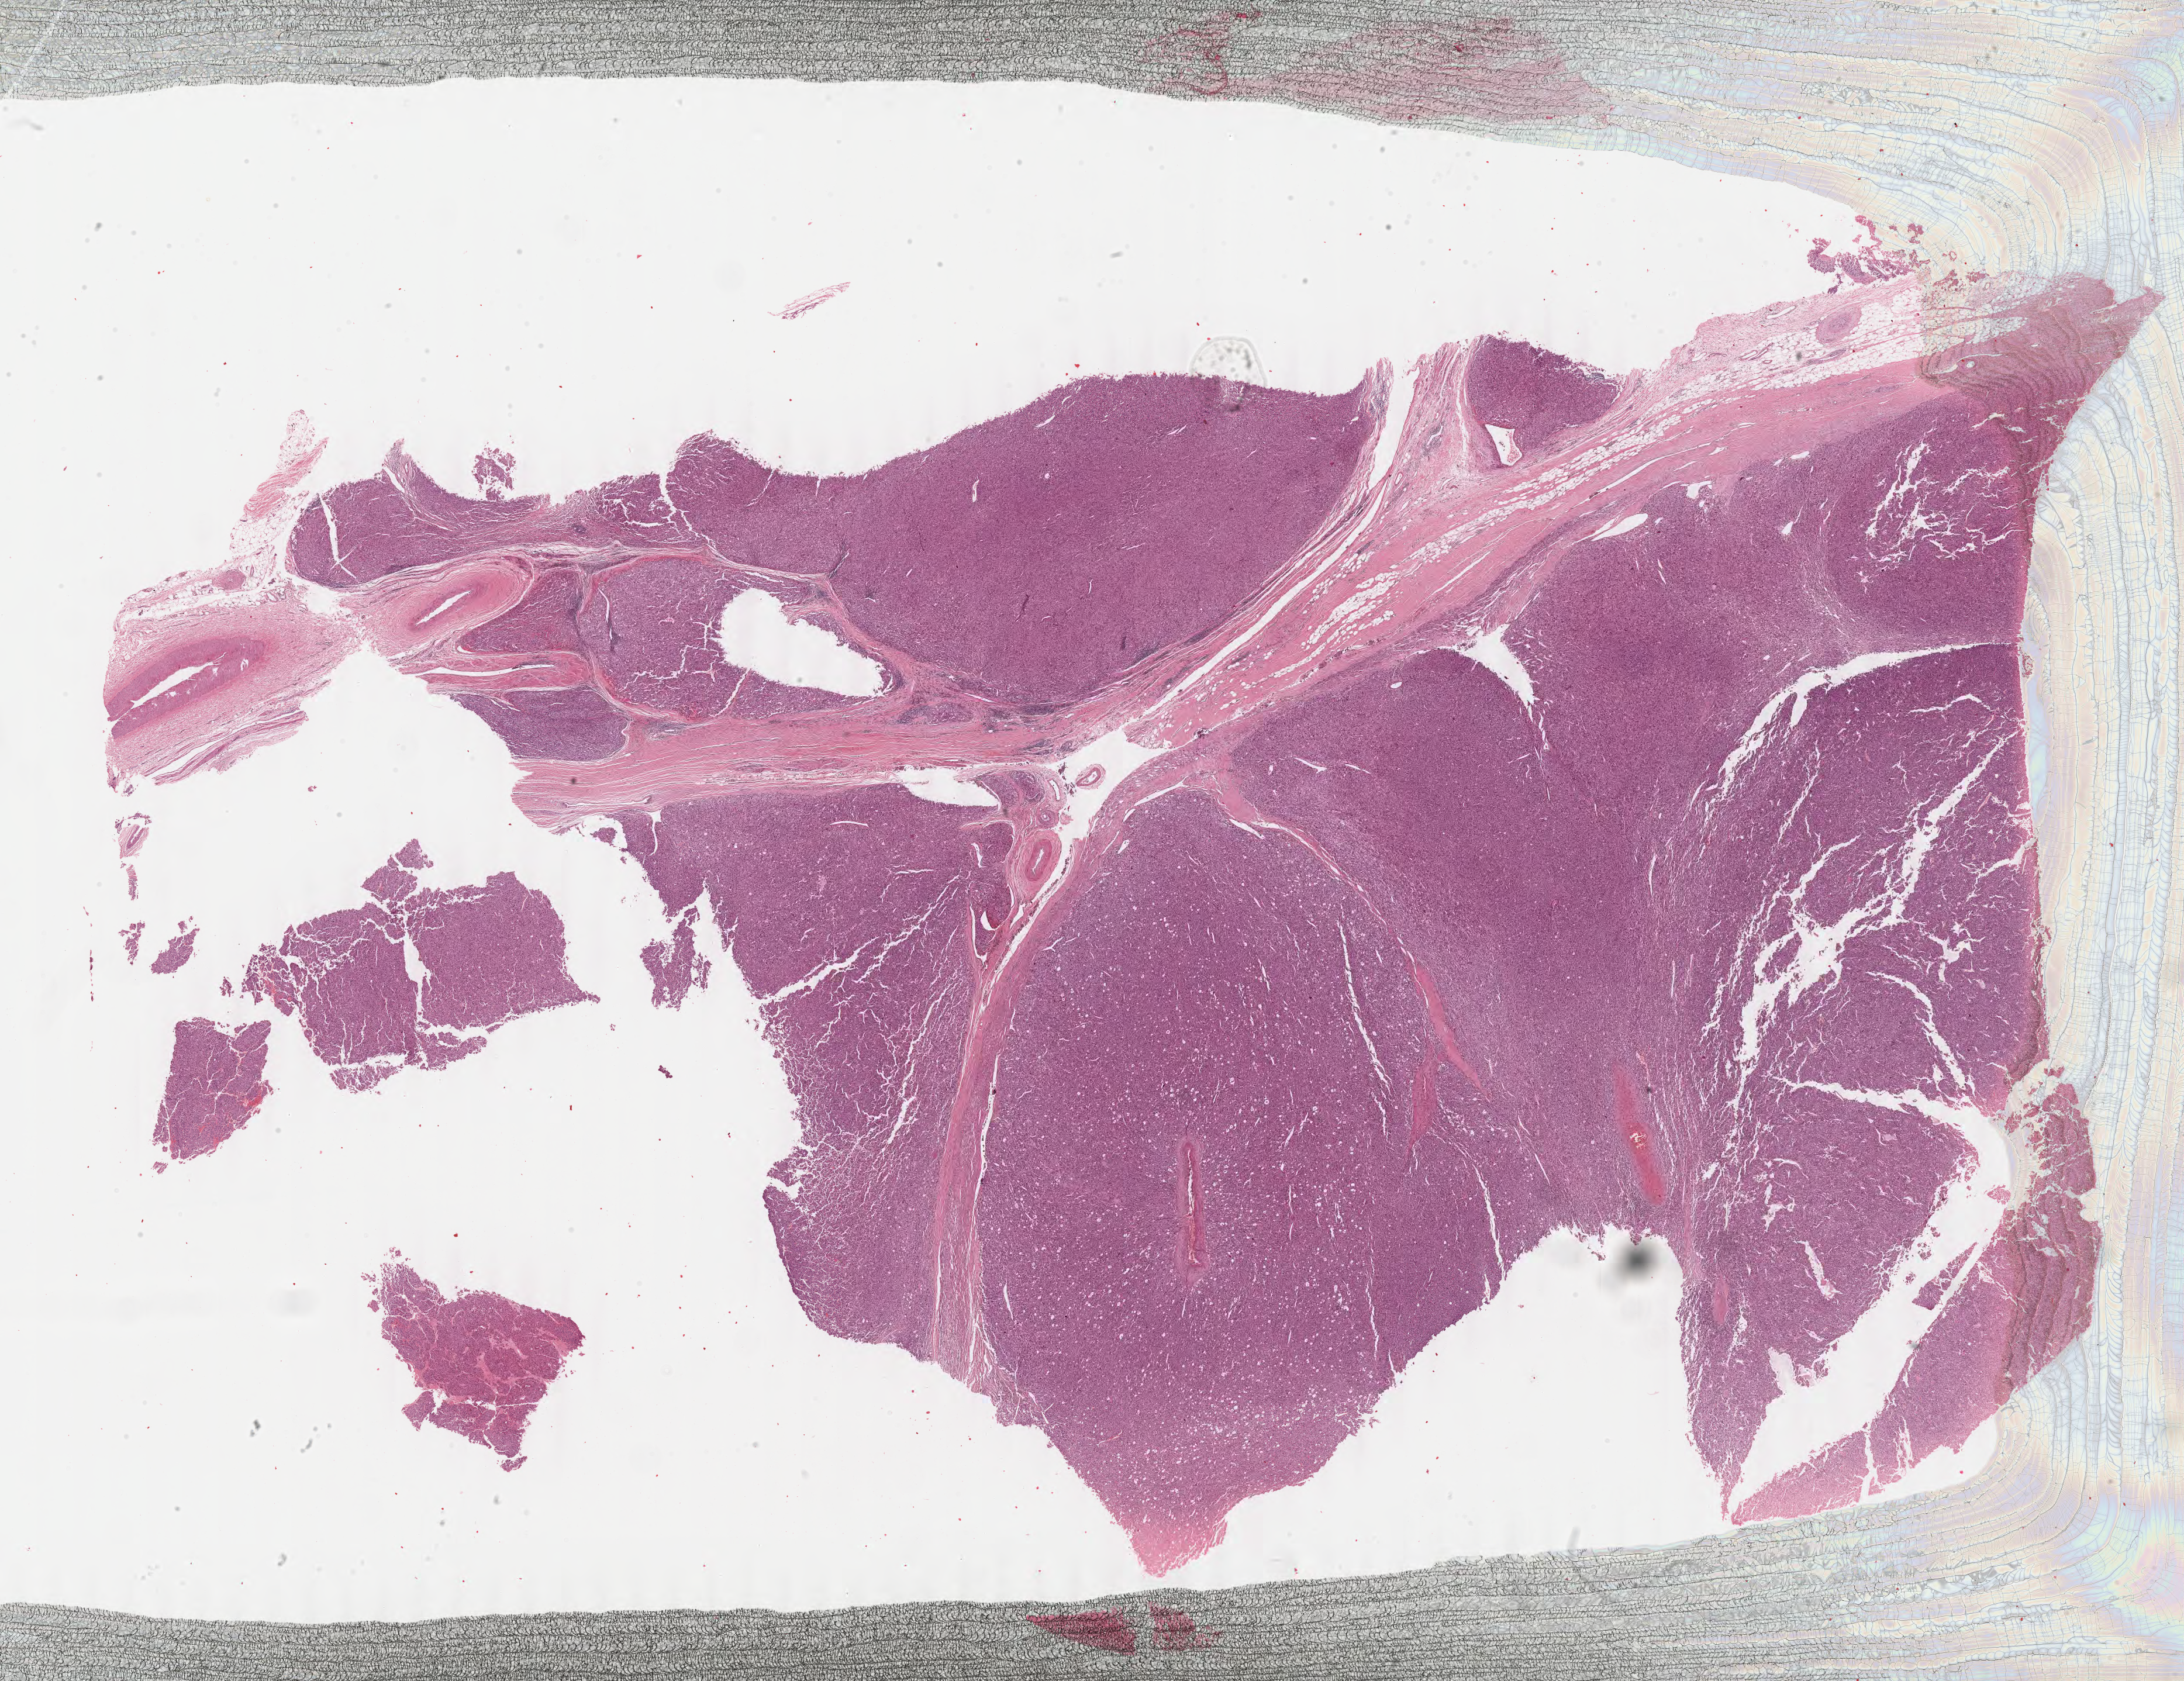
Digitized H&E tissue section (whole slide) — whole scanned area (about 29.5 x 22.7 mm, acquisition: 40x scan) shown as a low-resolution overview; formalin-fixed paraffin-embedded (FFPE) diagnostic section; sample: primary tumour, adrenal cortex. Male patient; age at initial diagnosis 63 years.
Pathologic diagnosis: Adrenal cortical carcinoma (cortex of adrenal gland).